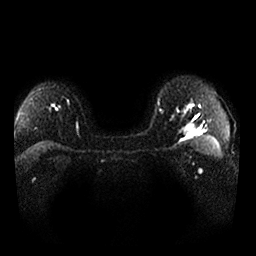
Breast MRI, one axial slice; position 14 of 25 along the scan axis; diffusion-weighted series; image 2 of 4 stored at this slice position (different b-values; order by instance number); 1.5 T; 4 mm slice thickness; 256 × 256 image matrix. Female patient.
Structures marked on this image (outlined manually by an expert reader):
- tumour on diffusion-weighted imaging: bounding box (x1, y1, x2, y2) in pixels: (181, 121, 196, 136)